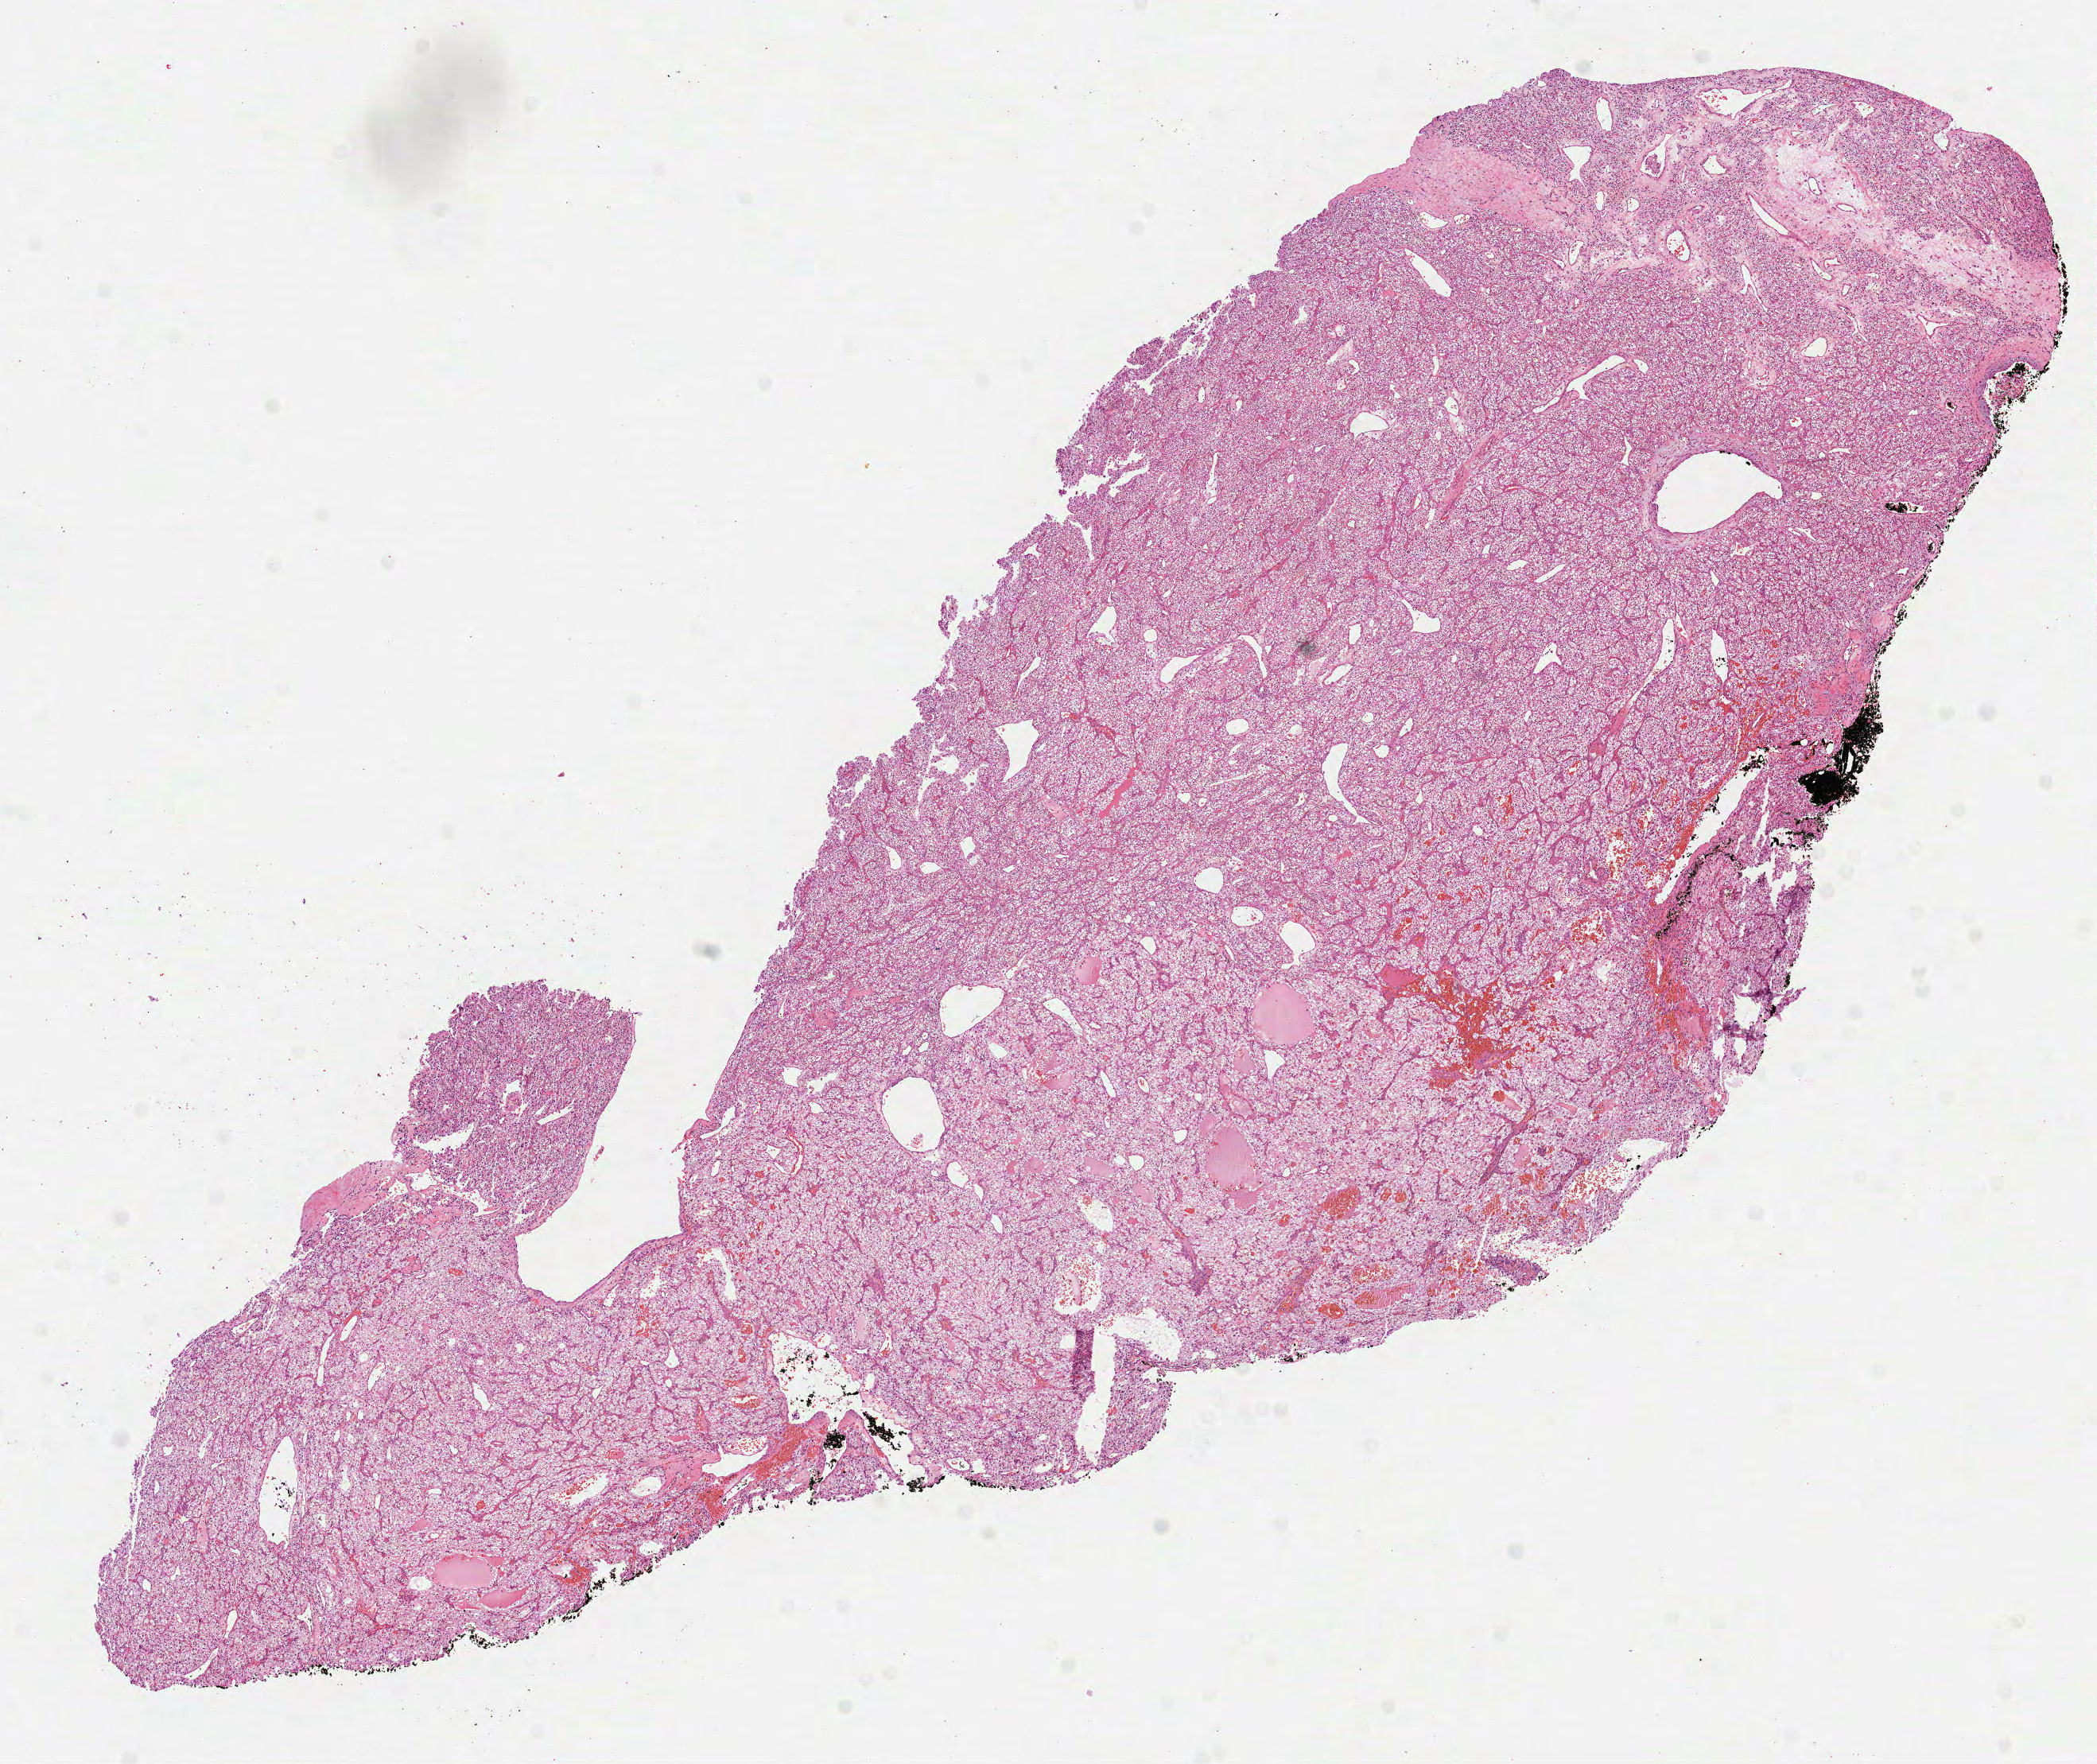
Whole-slide histology image, Hematoxylin and eosin (H&E) stained — a low-resolution overview of the entire scanned area, about 10.6 x 8.9 mm (acquisition: 40x scan); formalin-fixed paraffin-embedded (FFPE) diagnostic section; sample: primary tumour, kidney. Male patient; age at initial diagnosis 53 years. Histologic grade: G1 (well differentiated).
• histologic diagnosis: Clear cell adenocarcinoma, NOS
• AJCC pathologic stage: I